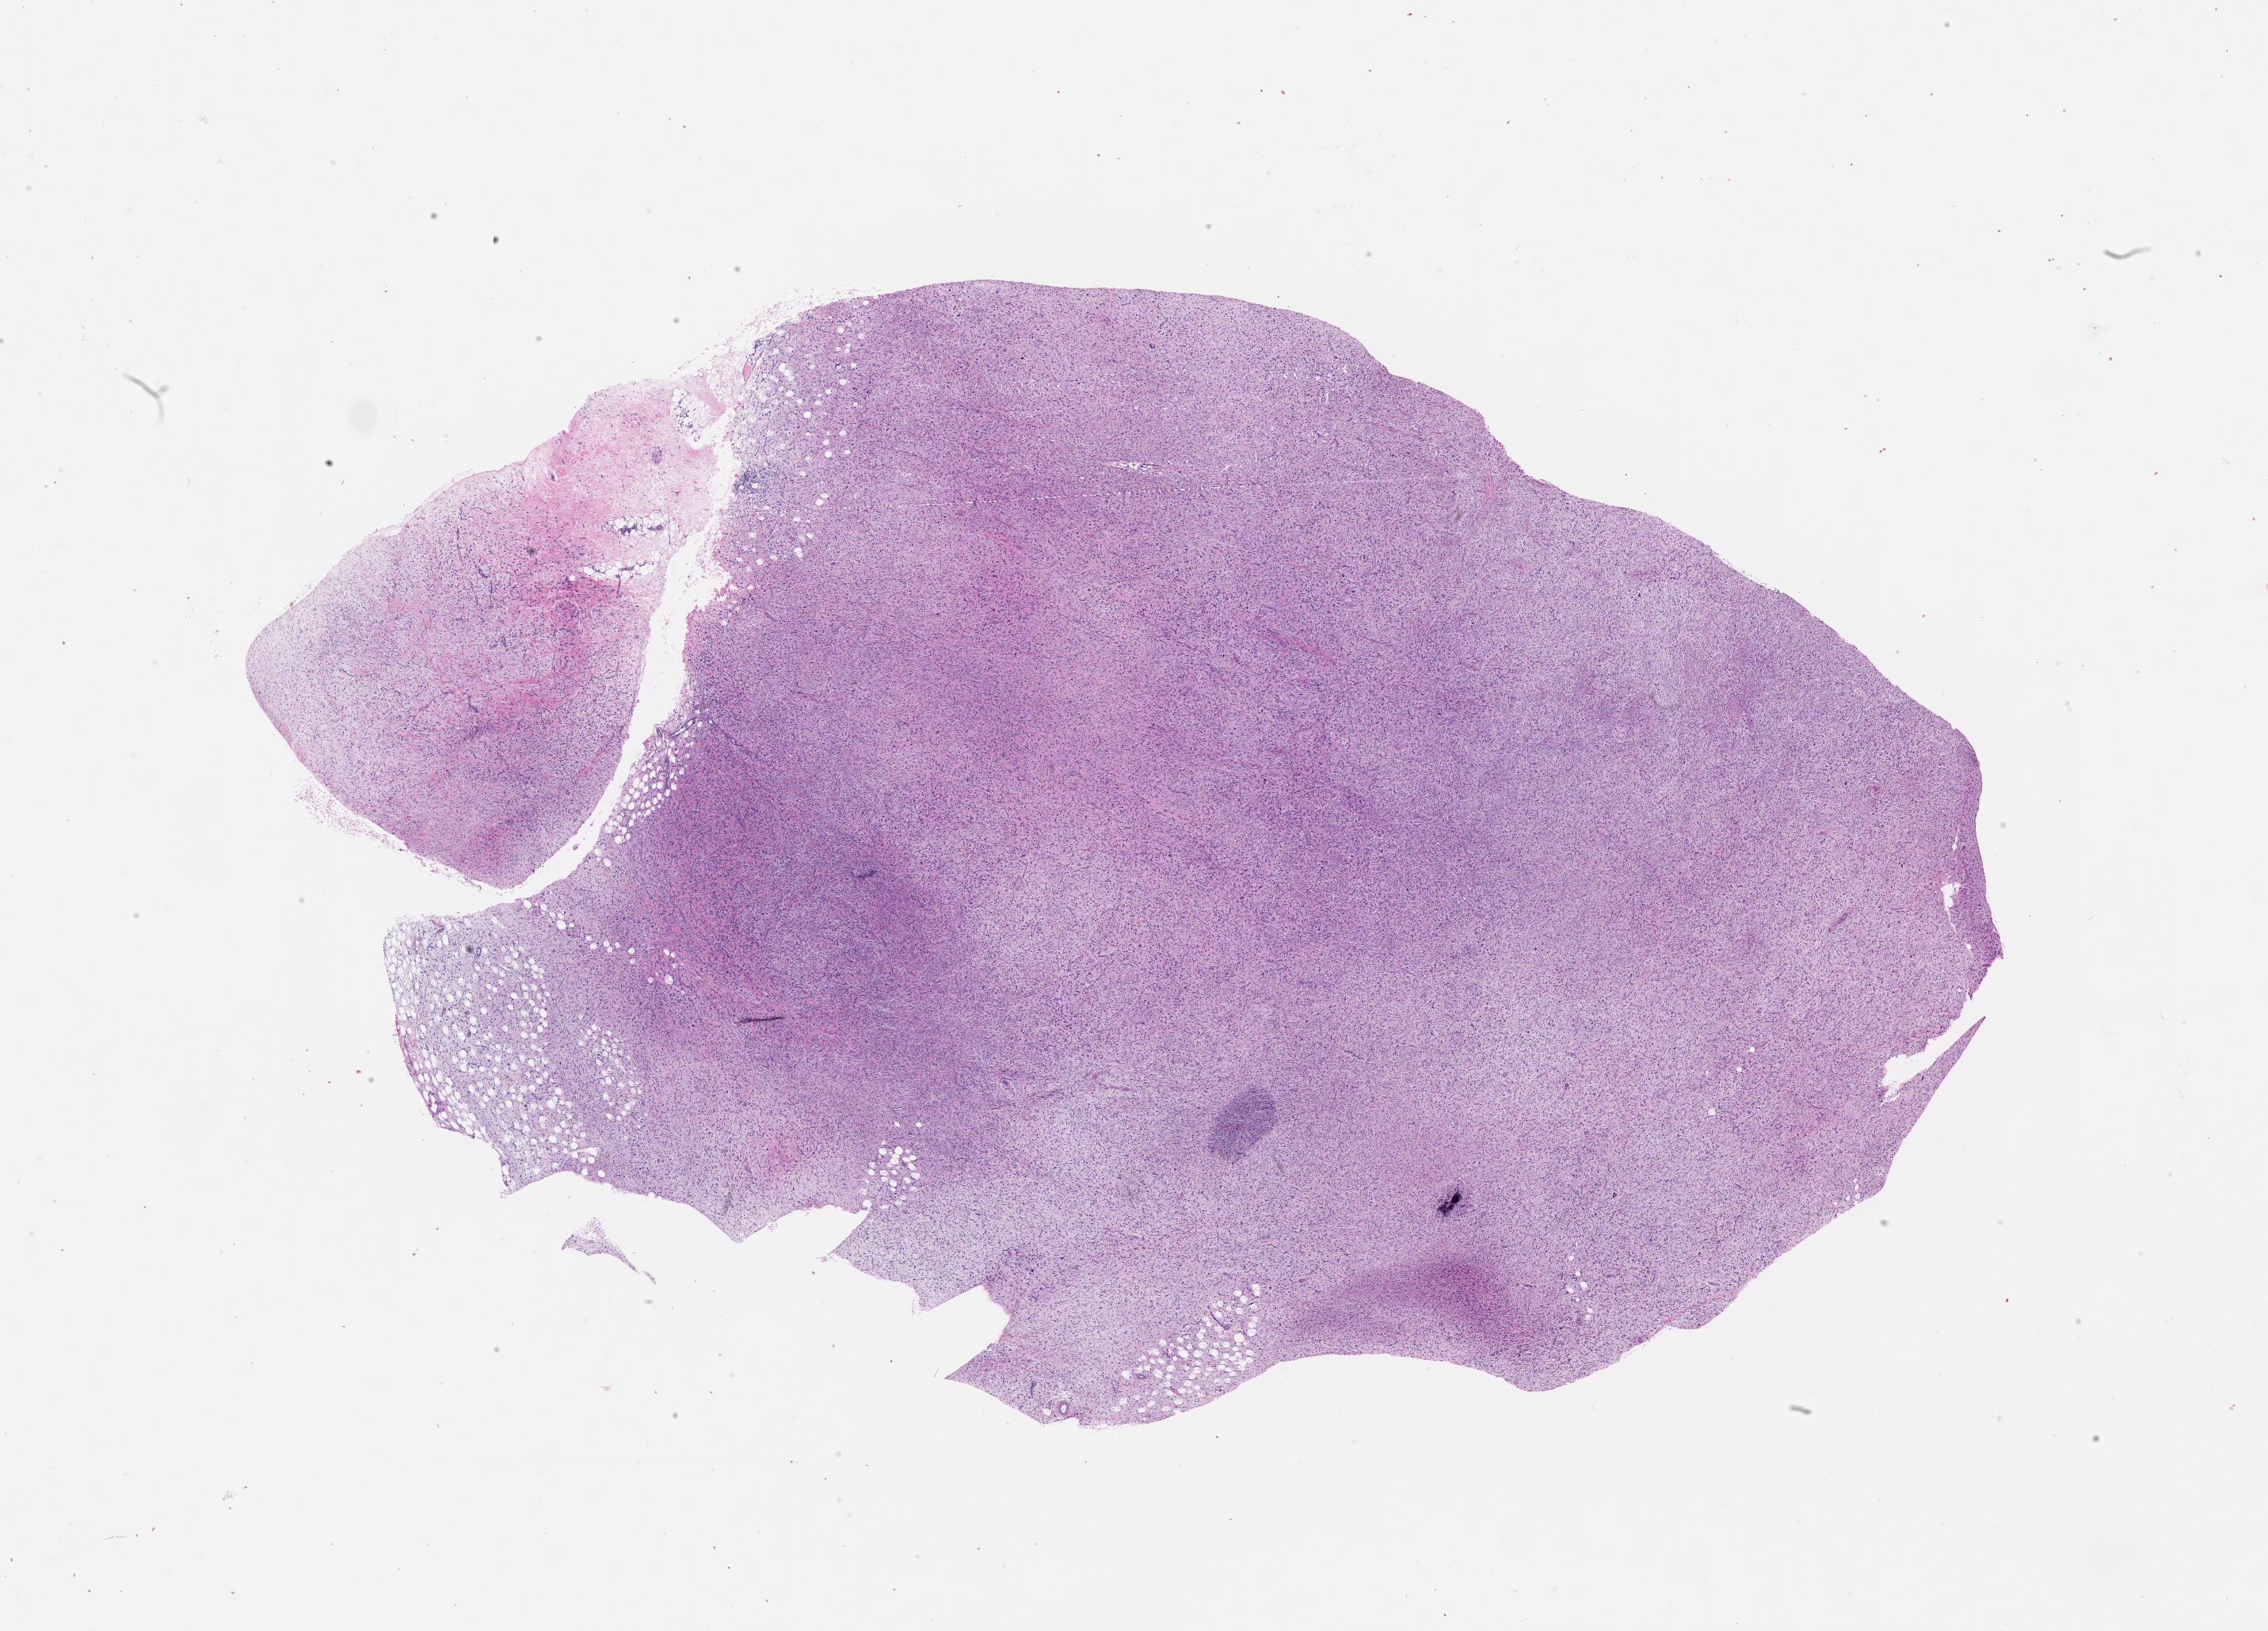
Digitized Hematoxylin and eosin (H&E) stained tissue section (whole slide) — shown as a low-resolution overview of the whole scanned area (about 23.1 x 16.6 mm).
• patient diagnosis (cohort enrolment): sarcoma (site not recorded at cohort level)